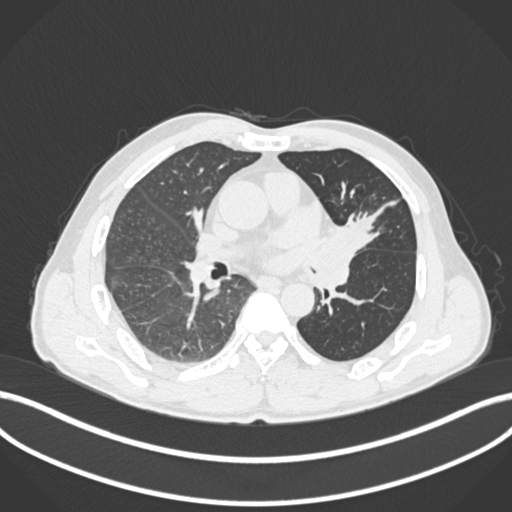
Chest CT, one axial slice; slice 98 of 255 in the series (ordered by position); lung window (W 1500 / L -600 HU); 512 × 512 image matrix. Male patient, age 57 years. From the clinical record (not read from this slice): clinical TNM (as recorded): T2b N0 M0.
Outlined on this slice (bounding box drawn by a radiologist):
- lung tumour (recorded histology: squamous cell carcinoma): bounding box <322,216,380,258> (left, top, right, bottom; pixels)